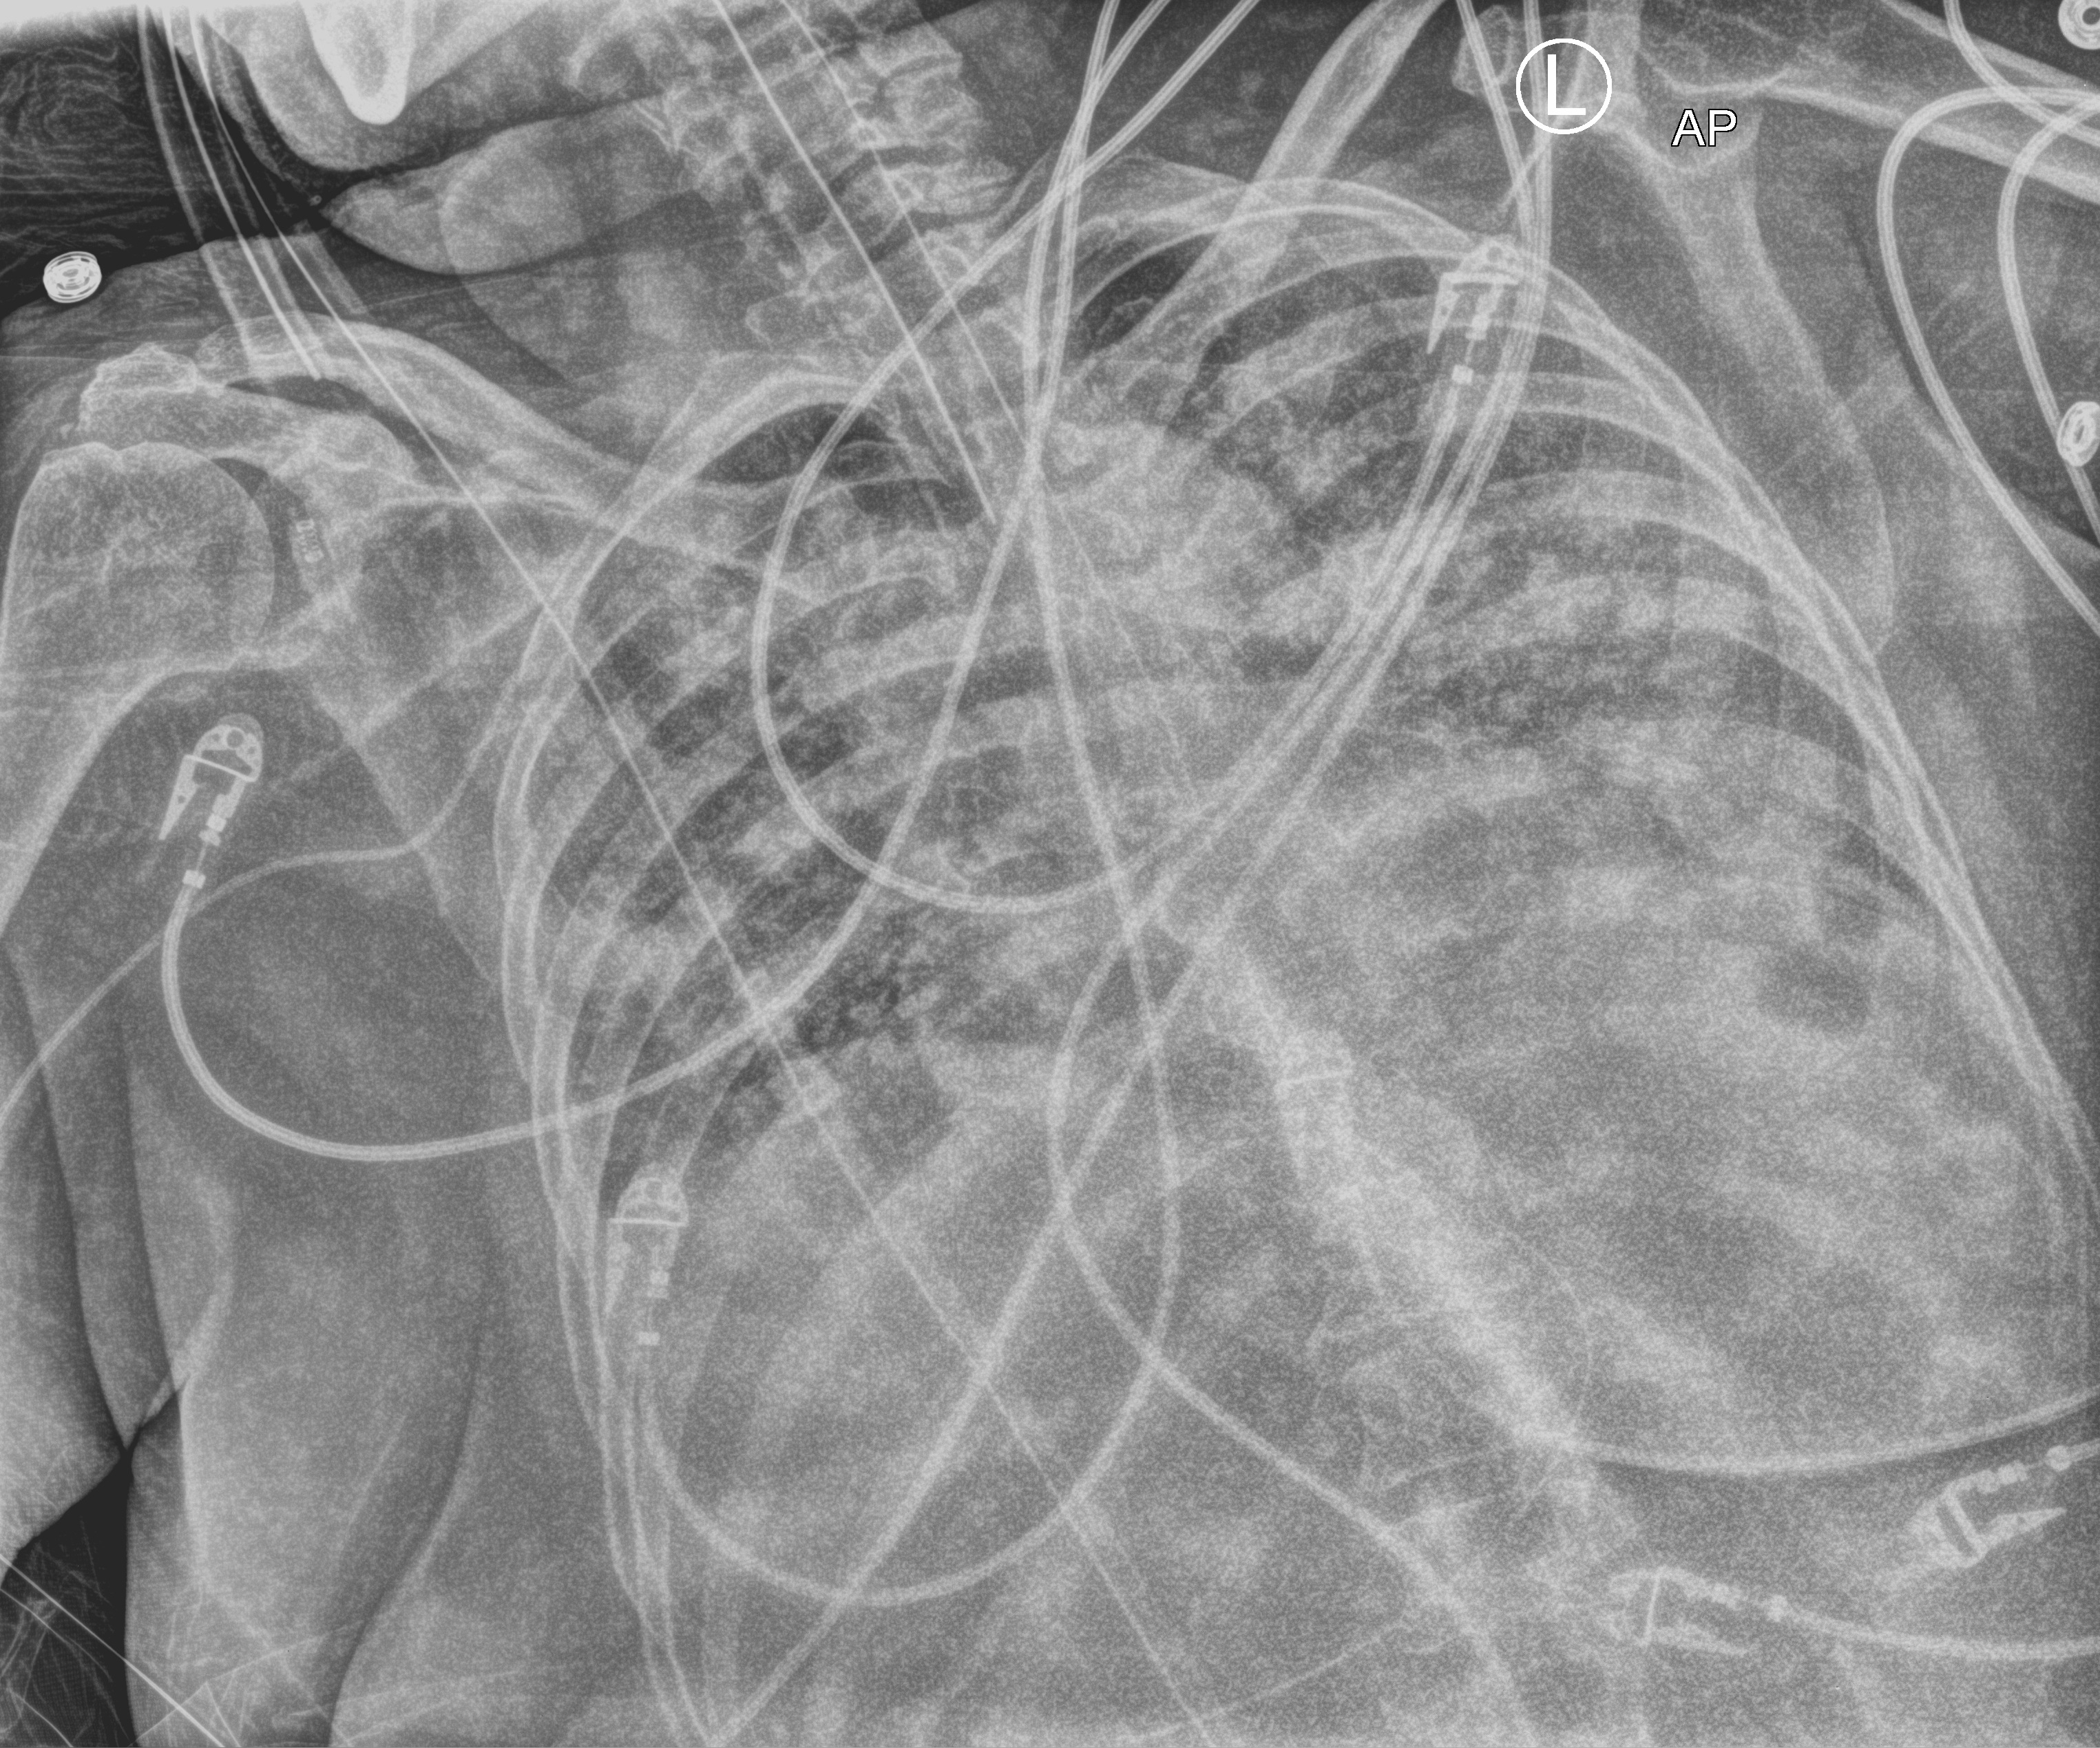
Chest X-ray (portable); anteroposterior (AP) projection. Patient hospitalised with COVID-19; female, aged 75–90 years.
Admission-level facts for this patient (not findings on this image; timing relative to this image not recorded):
- admitted to intensive care during this hospital stay: yes
- mechanically ventilated during this hospital stay: yes
- hypertension (admission record): yes